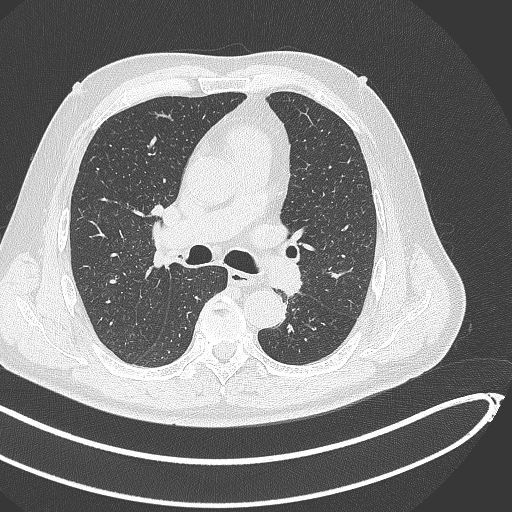
Chest CT, one axial slice. Position 280 of 468 along the scan axis. Lung window (W 1500 / L -600 HU). 1 mm slice thickness. 512 × 512 image matrix, field of view 400 × 400 mm. Patient: male, 64 years. From the clinical record (not read from this slice): clinical TNM (as recorded): T1c N0 M0; histopathological grade: G2.
Structures marked on this image (rectangle marked by the reading radiologist):
- lung tumour (recorded histology: squamous cell carcinoma): bounding box <263,252,308,300> (left, top, right, bottom; pixels)